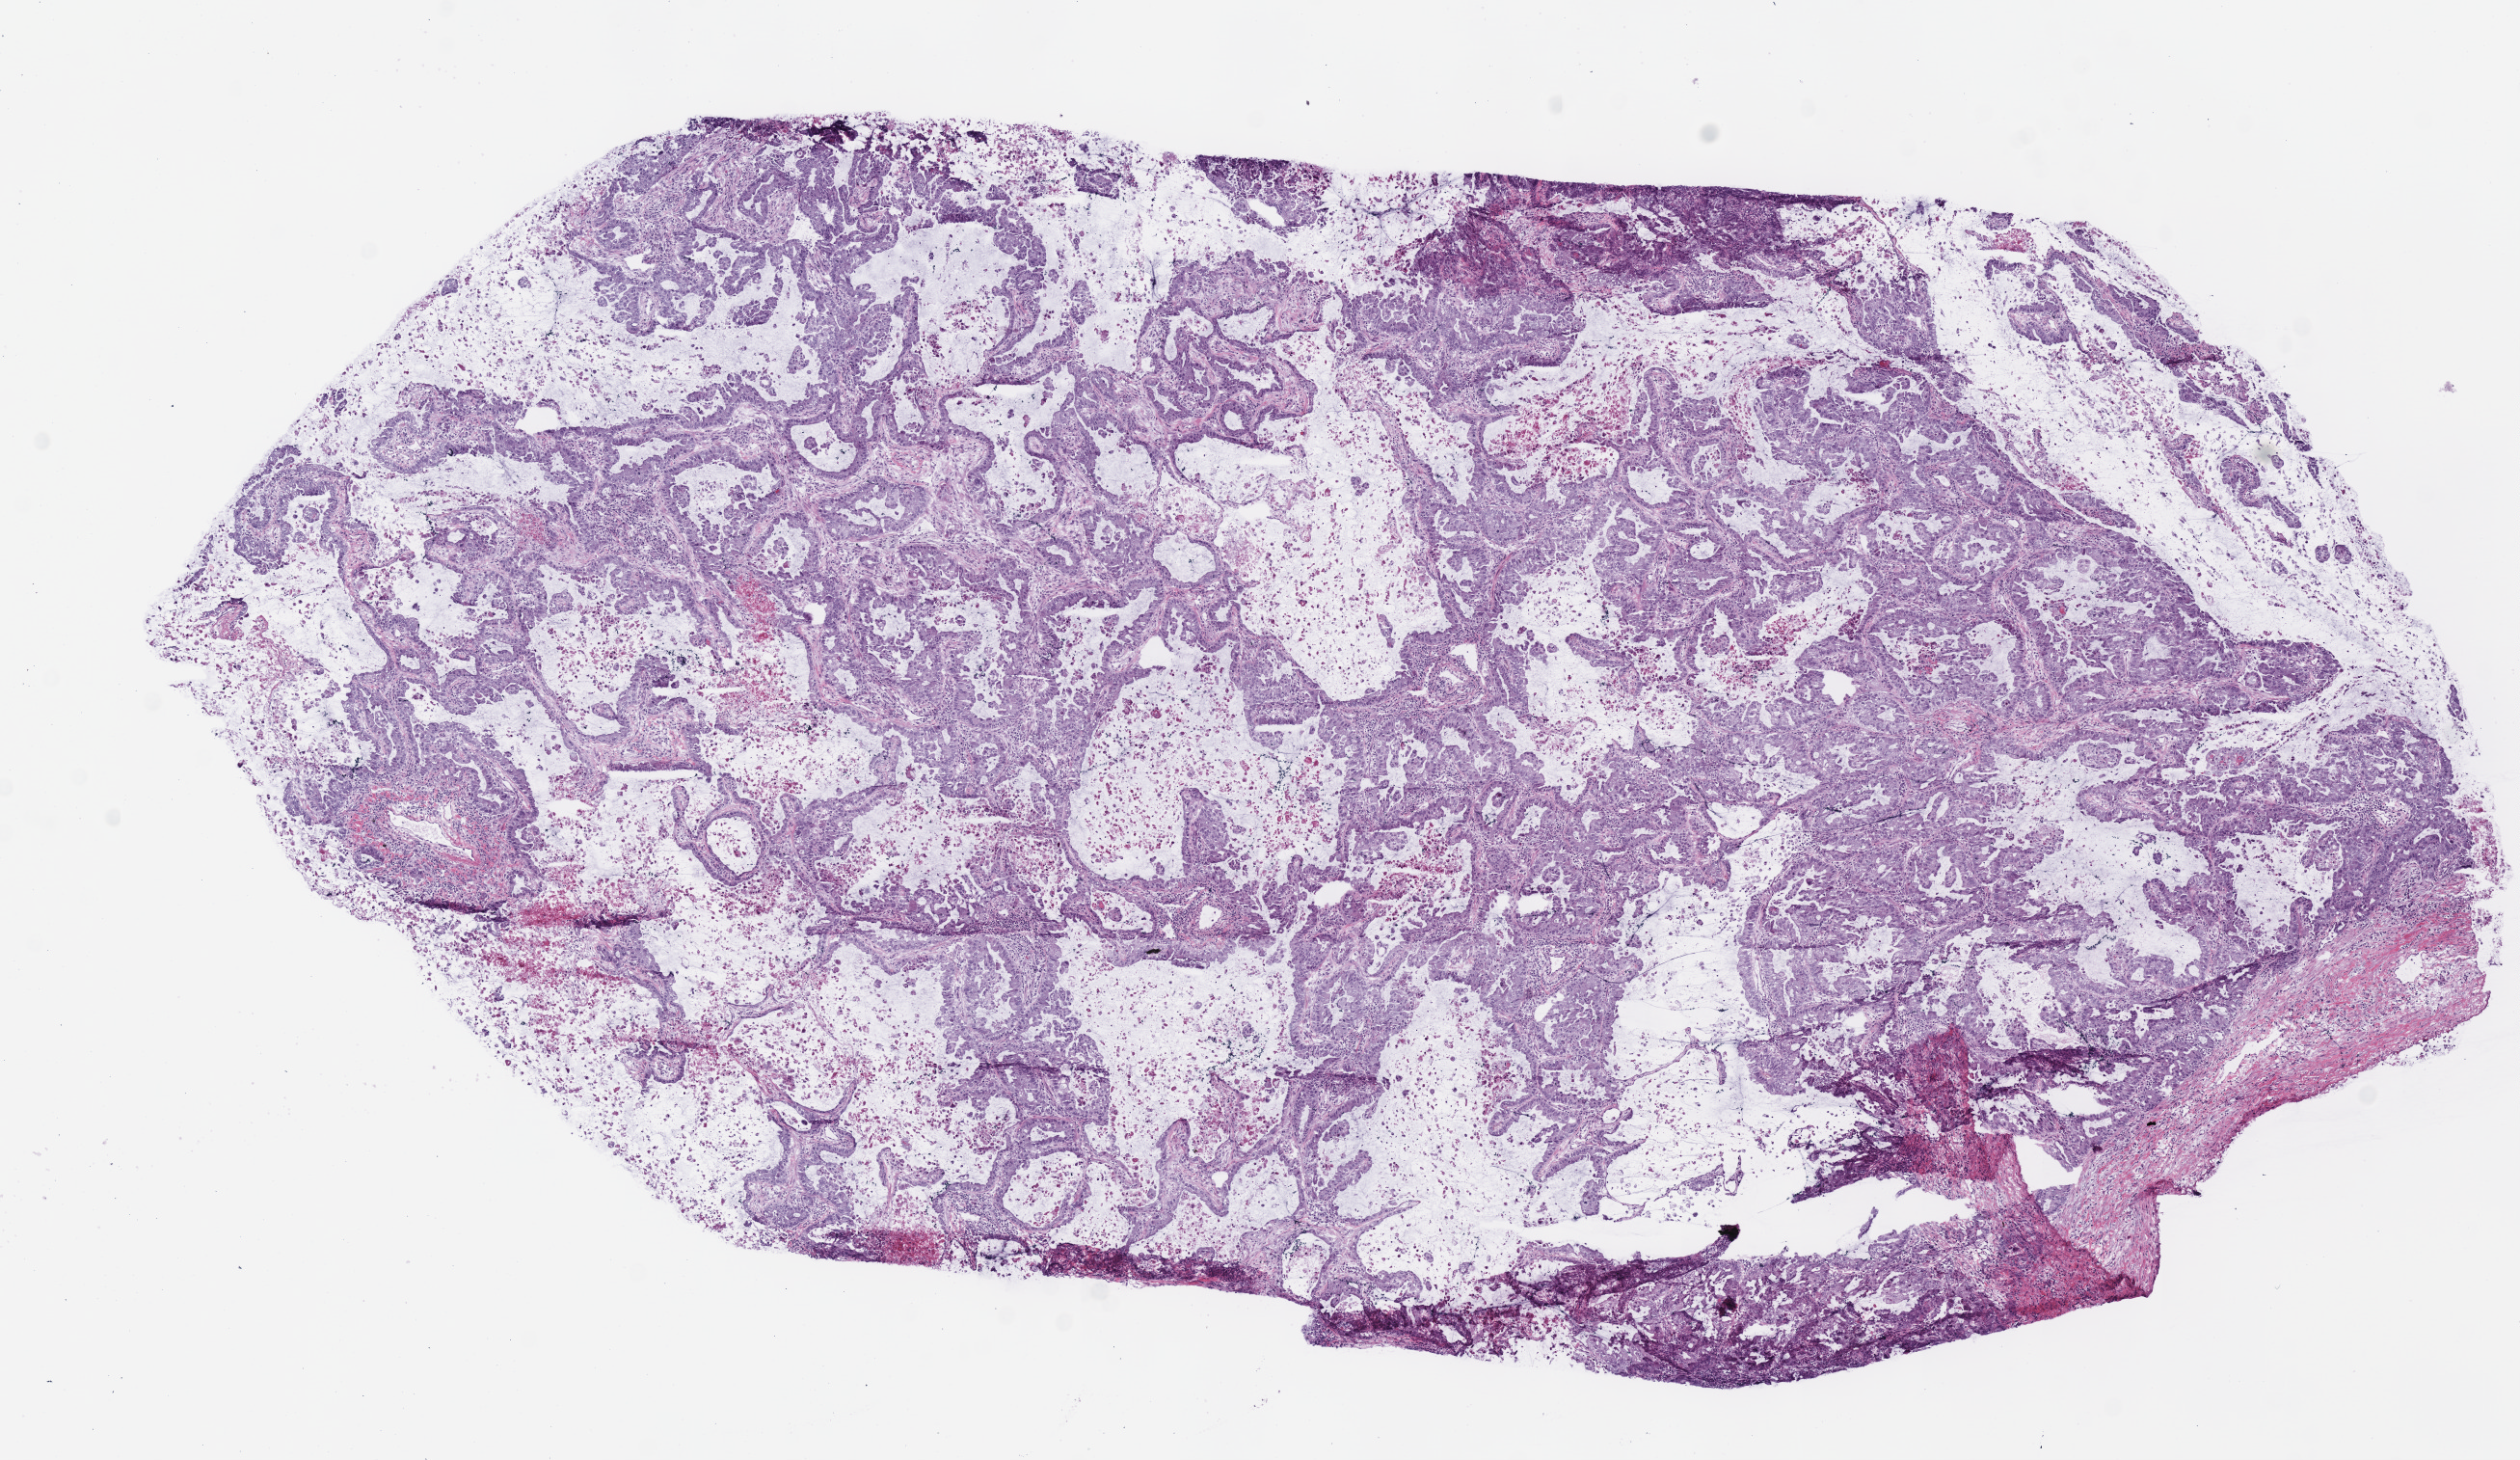
Whole-slide histology image, Hematoxylin and eosin (H&E) stained, low-resolution overview of the scanned area, about 10.3 x 6.0 mm (acquisition: 40x scan), frozen section from the bottom of the tissue portion, sample: primary tumour, lung. Male patient; age at initial diagnosis 55 years. Pathologist review of this section (percent, as recorded): tumour cells 94%, tumour nuclei 75%.
Diagnosis: Adenocarcinoma with mixed subtypes (lower lobe, lung).